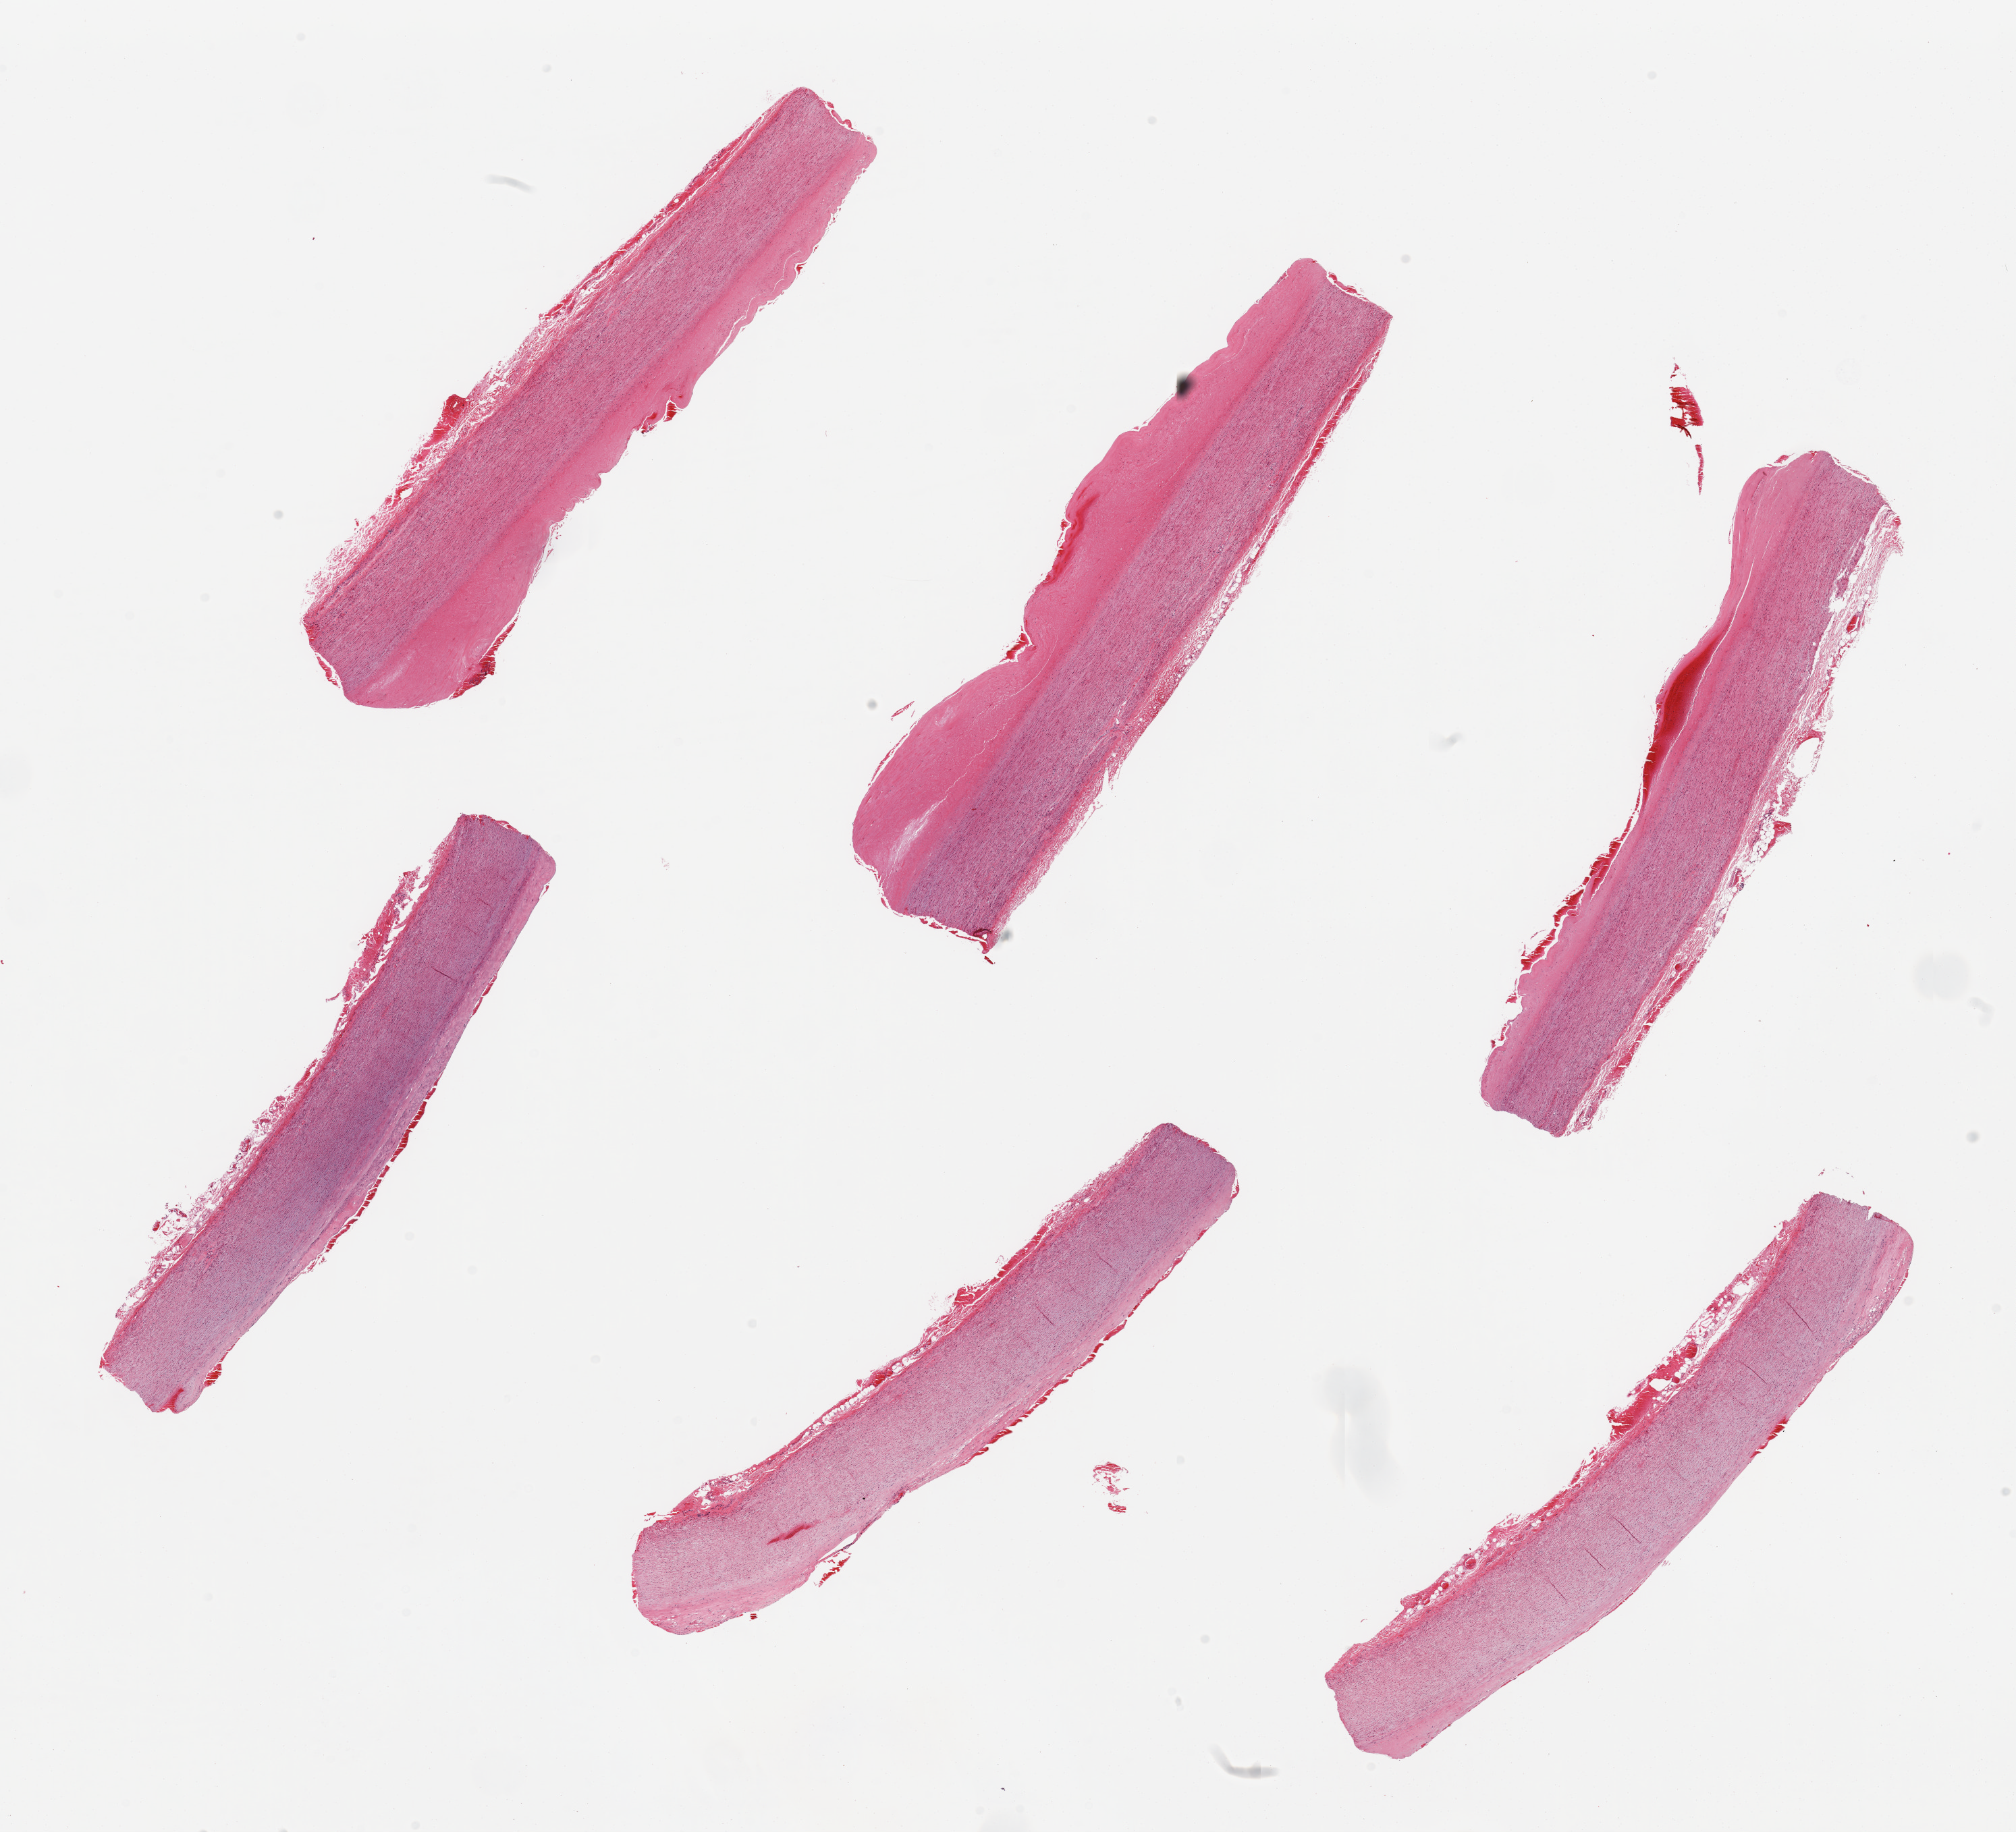
Haematoxylin and eosin whole-slide image, shown as a low-resolution overview of the whole scanned area (about 23.6 x 21.5 mm). PAXgene-fixed, paraffin-embedded tissue. Sampled site (target tissue): aorta. Tissue donor sample. Donor: male.
- pathologist's review note for this sample: 6 pieces. Flat fibrous plaque up to 1 mm thick on 3 pieces. Welll trimmed